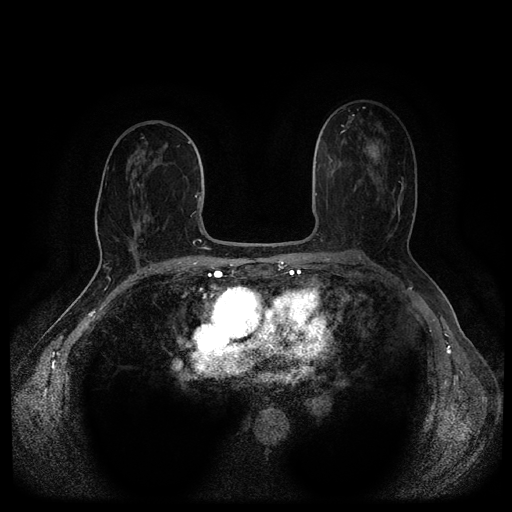
Breast MRI (dynamic contrast-enhanced, multi-phase), one axial slice; slice 58 of 116 in the series (ordered by position); dynamic contrast-enhanced series, time point 2 of 5 at this slice position (early post-contrast); 1.5 T; TE 2.6 ms, TR 5.4 ms; 2.1 mm slice thickness; 512 × 512 image matrix, field of view 340 × 340 mm. Female patient, age 69 years.
Outlined on this slice (semi-automatic segmentation, software-assisted and operator-edited):
- breast lesion (labelled benign in the annotation): bounding box [x1, y1, x2, y2] px = [363, 139, 383, 167]